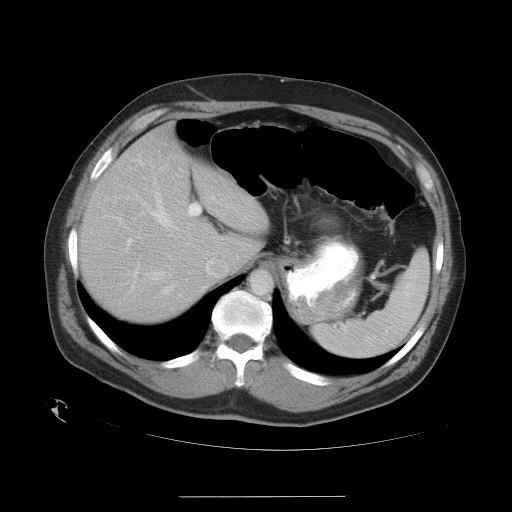
Contrast-enhanced abdominal CT, one axial slice. Slice 24 of 35 in the series (ordered by position). Reconstruction kernel STANDARD. 120 kVp. Soft-tissue window (W 400 / L 40 HU). 7.5 mm slice thickness. 512 × 512 image matrix, field of view 450 × 450 mm. Male patient, age 67 years. From the clinical record (not read from this slice): diagnosis: colorectal cancer liver metastases, imaged before liver resection; multiple liver metastases: no; largest metastasis: 2.3 cm.
Annotated regions visible in this slice (expert manual segmentation):
- hepatic veins: box from (x=135, y=162) to (x=195, y=292) px
- liver: (x=81, y=126)–(x=266, y=323)
- planned liver remnant (the part of the liver to remain after resection): (x=88, y=126)–(x=266, y=323)
- portal vein (with intrahepatic branches): (x=114, y=195)–(x=220, y=284)